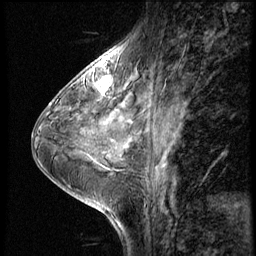
Breast MRI (dynamic contrast-enhanced), one sagittal slice. Position 23 of 56 along the scan axis. 4 images stored at this slice position (order not interpretable as contrast timing). 1.5 T. TE 4.2 ms, TR 8.9 ms. 2.5 mm slice thickness. 256 × 256 image matrix, field of view 200 × 200 mm. Patient: female, 38 years. Case-level facts recorded for this patient, not image findings: setting: breast cancer imaged before/during neoadjuvant chemotherapy; receptor status: triple-negative.
Outlined on this slice (semi-automatic segmentation, software-assisted and operator-edited):
- analysis volume of interest (the breast-tissue region the enhancement analysis was run in; not a lesion): bounding box [x1, y1, x2, y2] px = [88, 73, 115, 102]
- tumour enhancement mask (voxels above the 140 % enhancement threshold inside the analysis volume of interest): [94, 76, 110, 93]